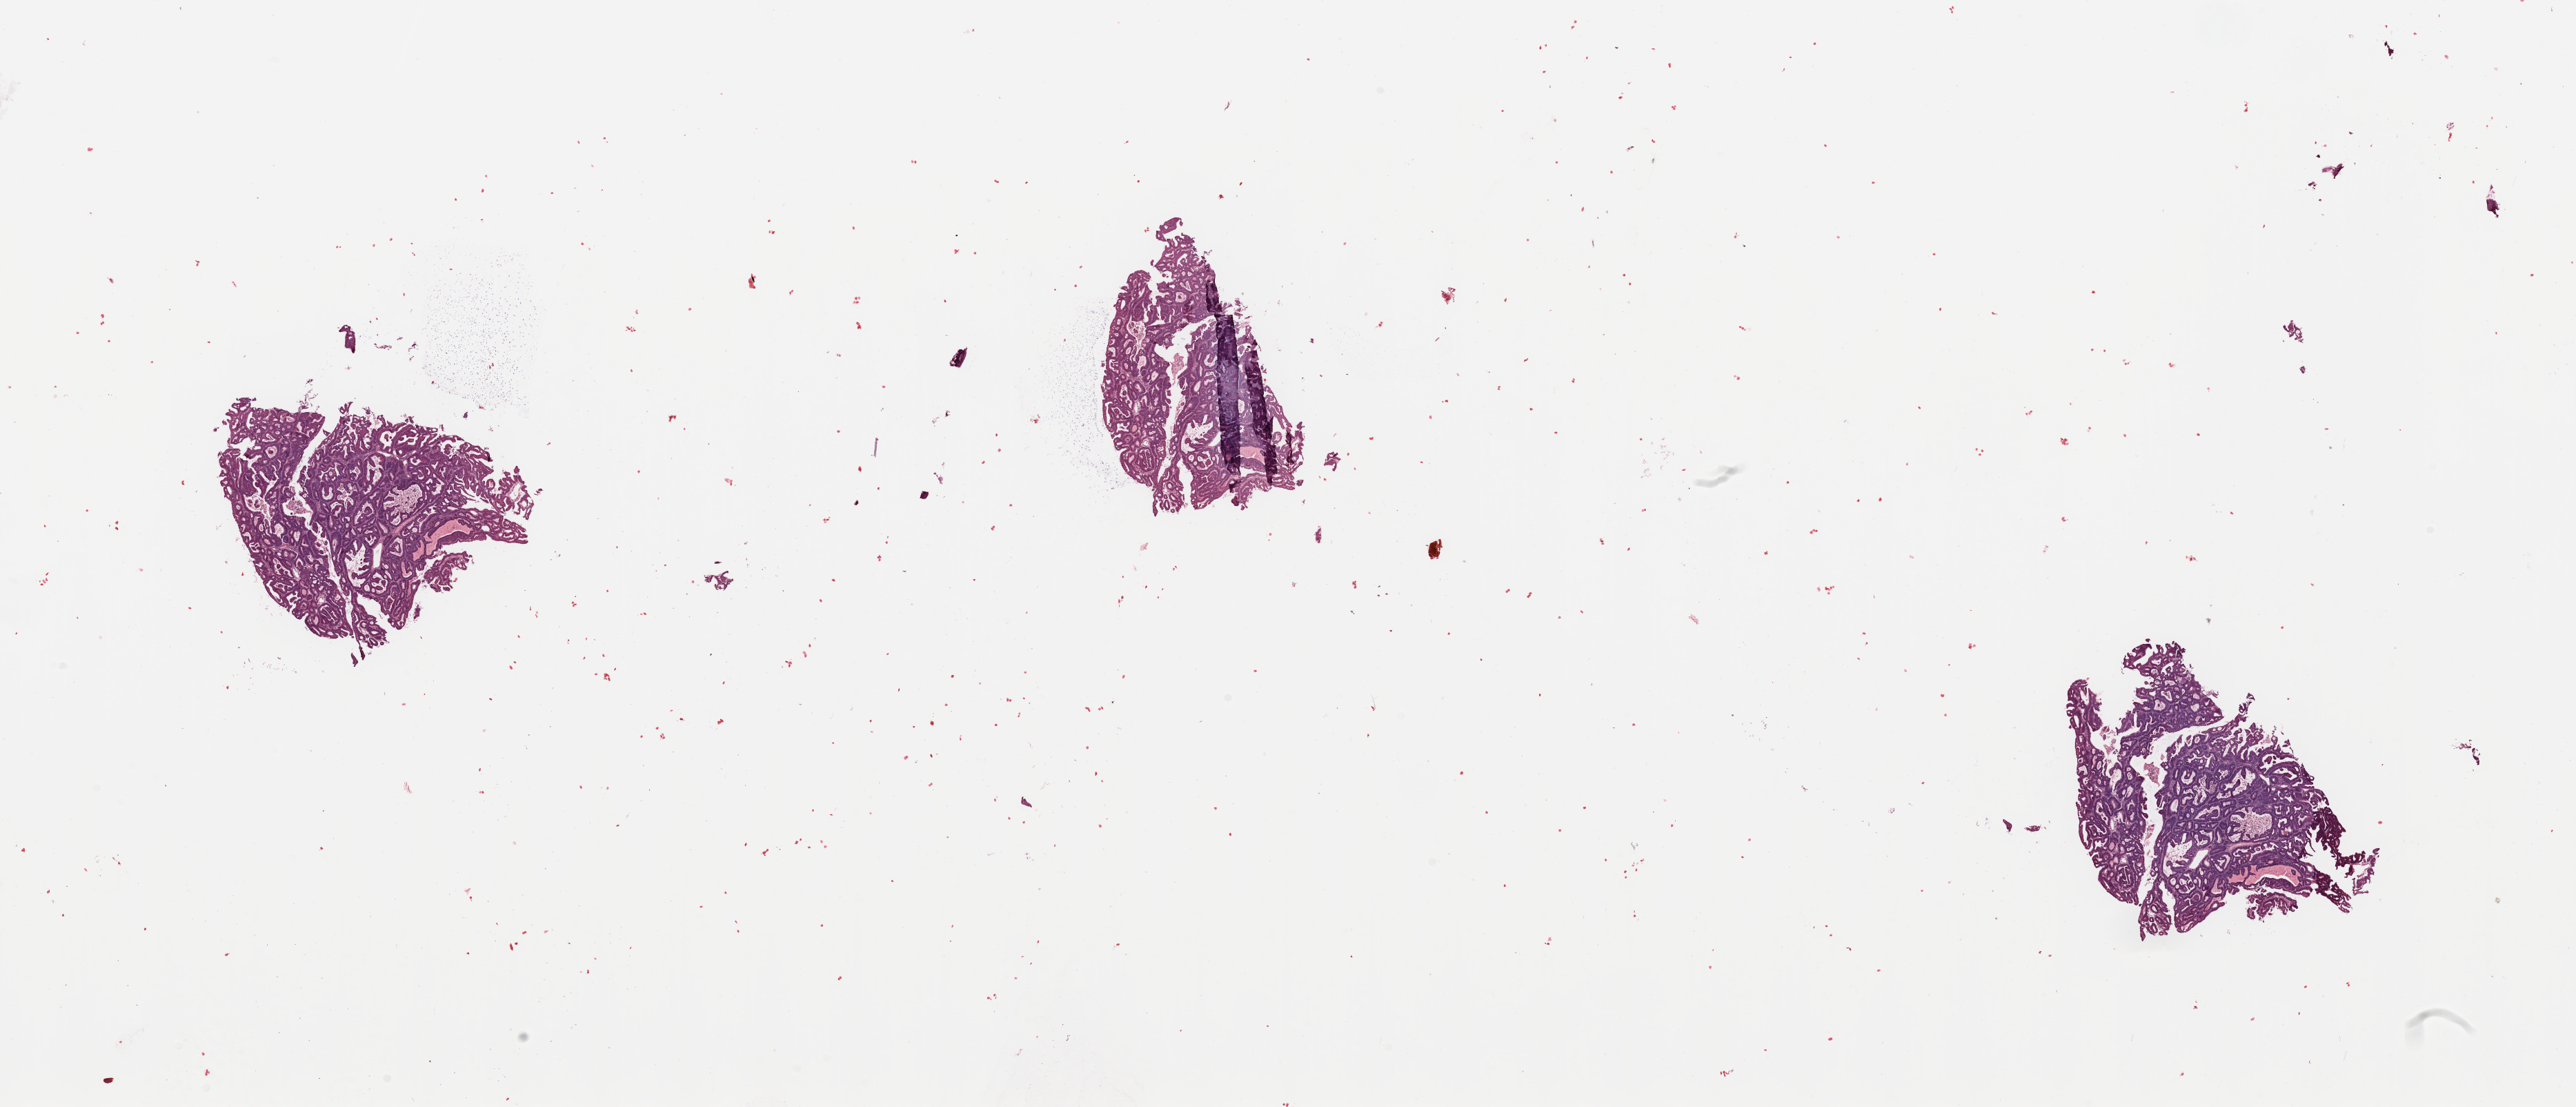
Whole-slide histology image, H&E-stained, a low-resolution overview of the entire scanned area, about 29.5 x 12.7 mm (acquisition: 20x scan), tumour tissue sample, sampled site: uterus. Female, 57 y/o. Histologic grade: G2 (moderately differentiated). Composition of this section per pathologist review: tumour nuclei 90%, necrosis 2%.
AJCC pathologic stage: I. Histologic diagnosis: Endometrioid adenocarcinoma, NOS. Primary tumour site (as recorded): anterior endometrium.